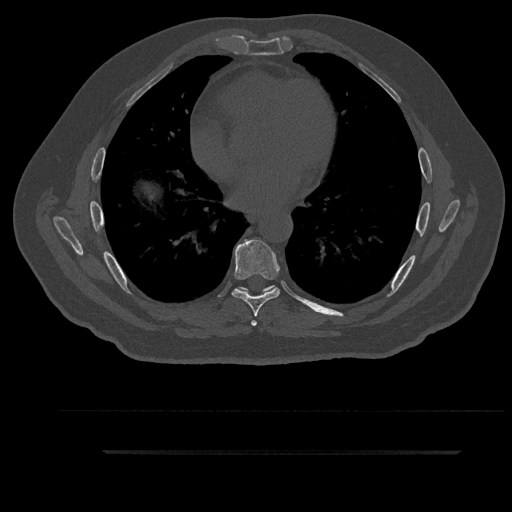
CT including the spine, one axial slice. Position 518 of 797 along the scan axis. Bone window (W 1800 / L 400 HU). 0.5 mm slice thickness. 512 × 512 image matrix. Male patient, age 63 years. From the clinical record (not read from this slice): primary cancer: renal.
Annotated regions visible in this slice (semi-automatic segmentation, software-assisted and operator-edited):
- T6 vertebra: bounding box [x1, y1, x2, y2] px = [236, 286, 275, 326]
- T7 vertebra: [232, 239, 281, 316]
- T8 vertebra: [241, 285, 274, 291]